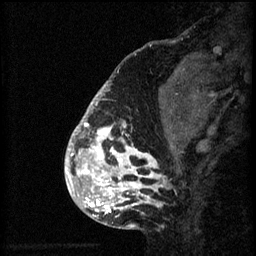
Breast MRI (dynamic contrast-enhanced), one sagittal slice. Slice 18 of 60 in the series (ordered by position). 3 images stored at this slice position (order not interpretable as contrast timing). 1.5 T. TE 4.2 ms, TR 8.2 ms. 2 mm slice thickness. 256 × 256 image matrix, field of view 180 × 180 mm. Female patient, age 41 years.
Outlined on this slice (semi-automatically segmented with operator editing):
- analysis volume of interest (the breast-tissue region the enhancement analysis was run in; not a lesion): bounding box (x1, y1, x2, y2) in pixels: (72, 108, 176, 205)
- tumour enhancement mask (voxels above the 70 % enhancement threshold inside the analysis volume of interest): (72, 108, 167, 205)